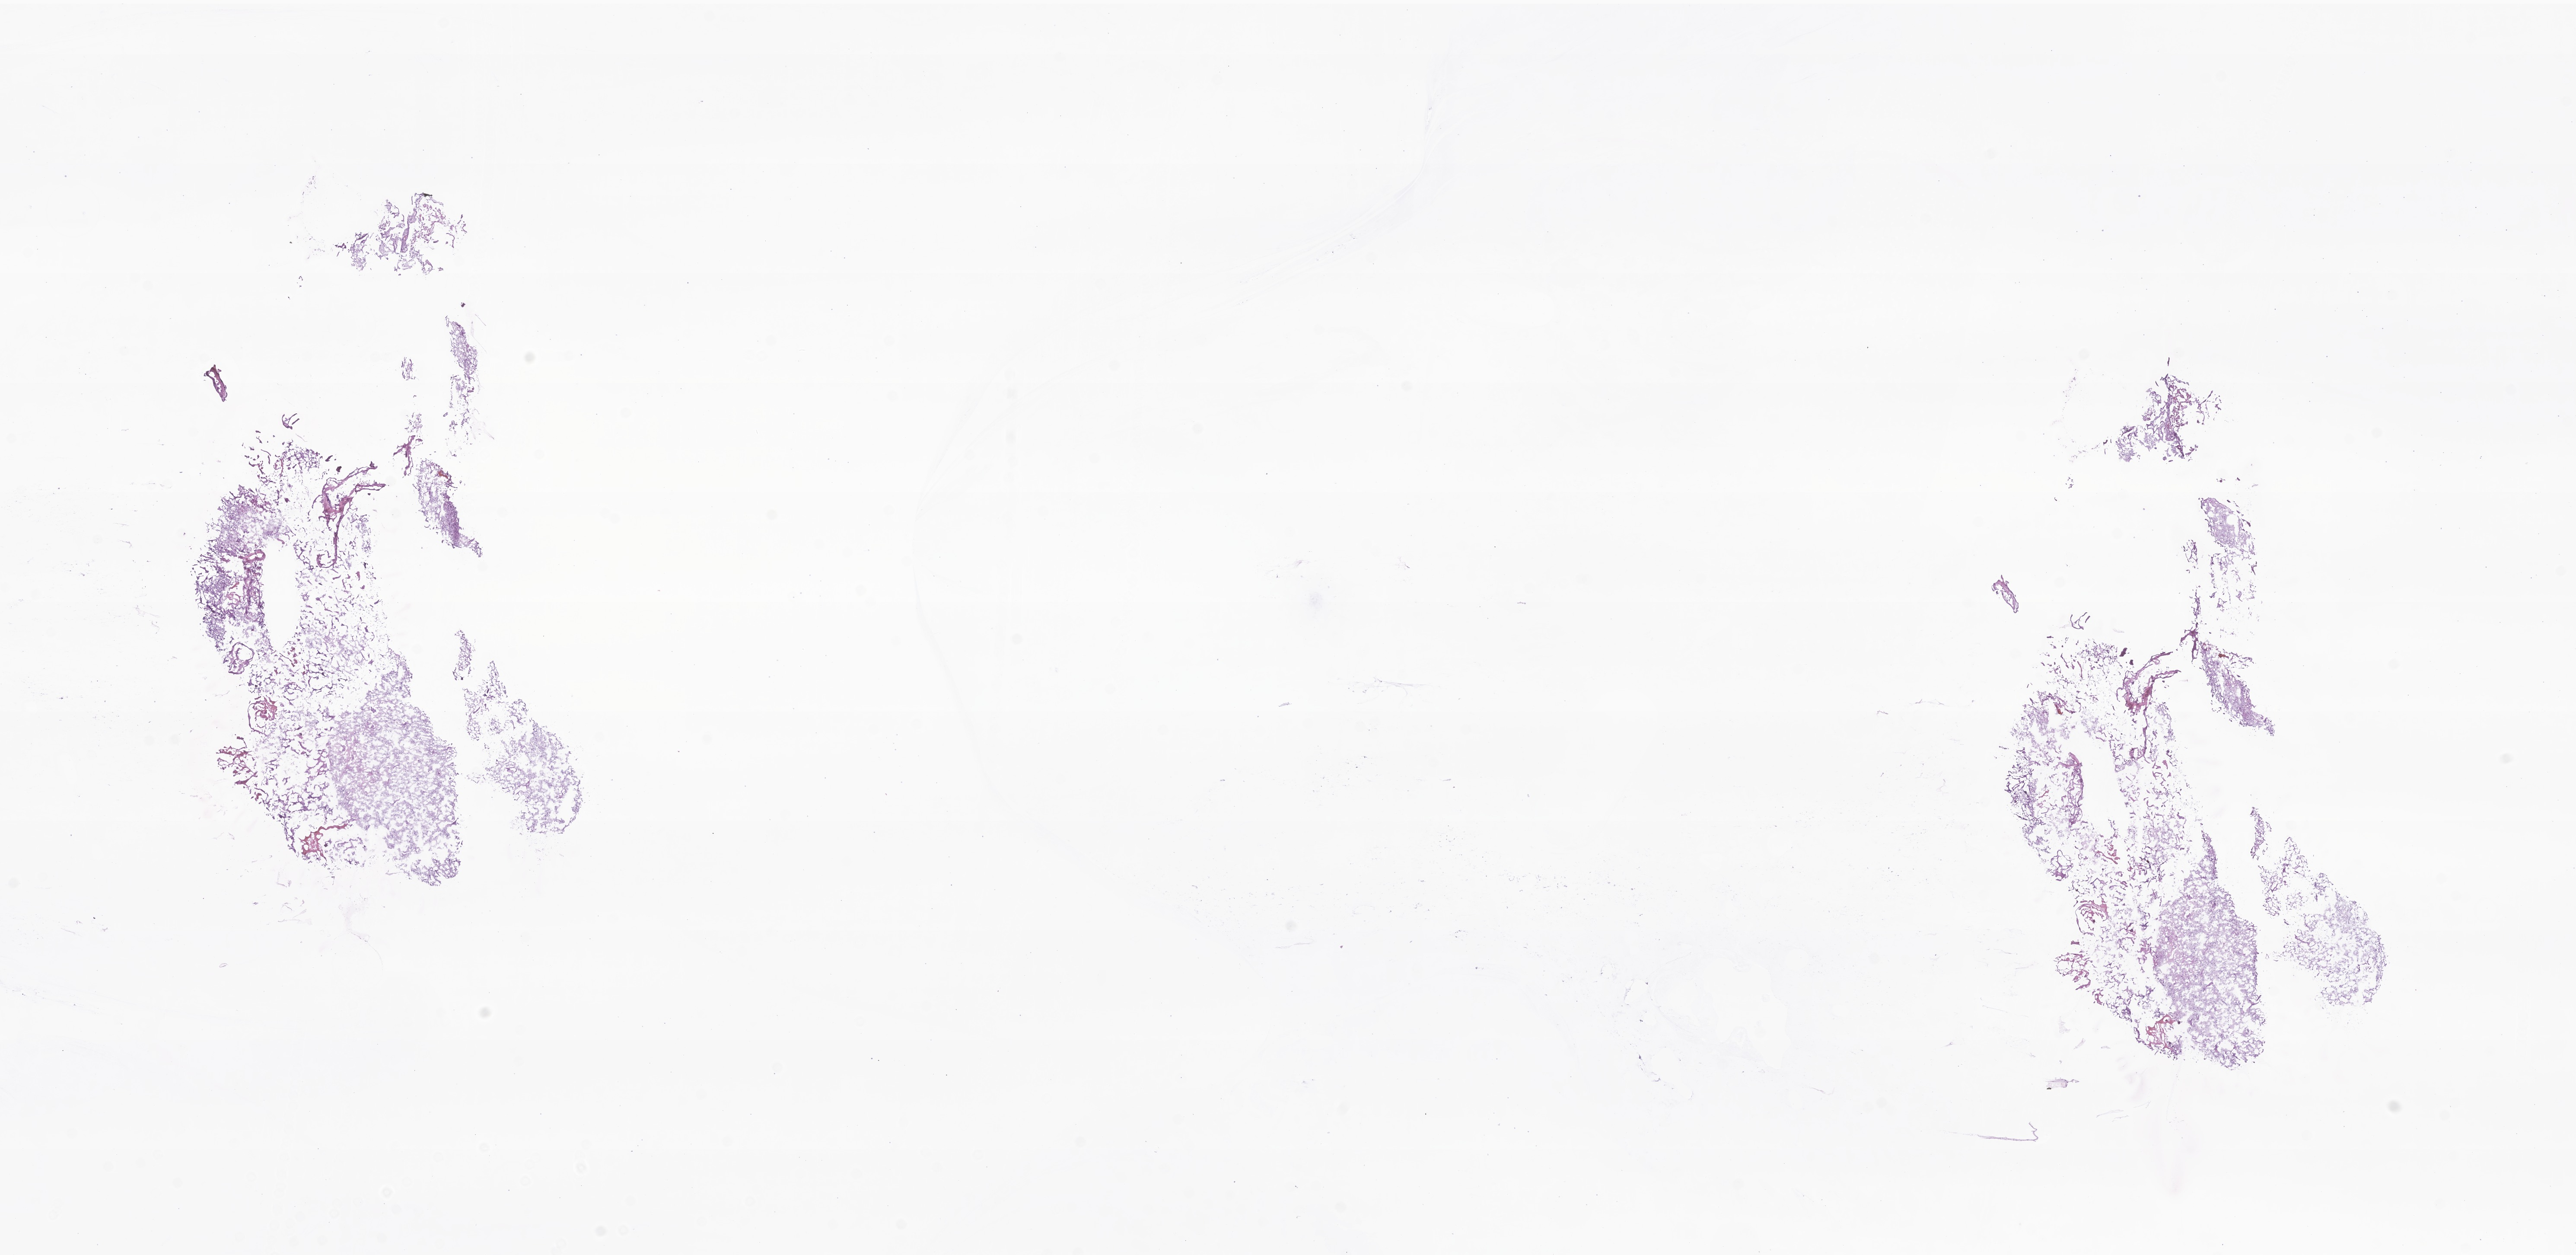
Whole-slide image, haematoxylin and eosin stain of tumor tissue from the brain — low-resolution overview of the scanned area, about 25.1 x 12.2 mm, frozen section. Male patient, age 102 months (8 years 6 months).
- diagnosis: Glioma, malignant